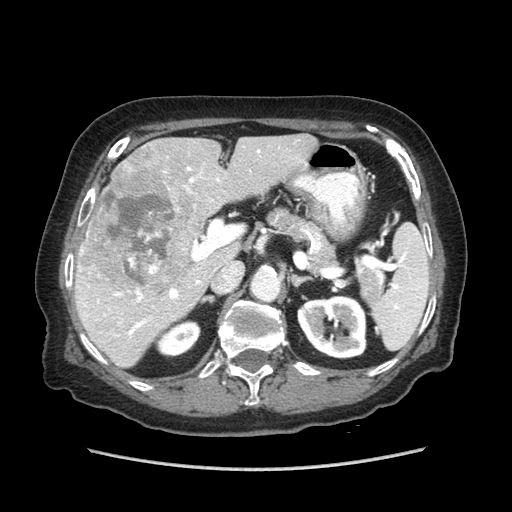
Contrast-enhanced abdominal CT (liver protocol), one axial slice. Slice 45 of 89 in the series (ordered by position). 140 kVp. Soft-tissue window (W 400 / L 40 HU). 2.5 mm slice thickness. 512 × 512 image matrix. Case-level facts recorded for this patient, not image findings: diagnosis: hepatocellular carcinoma (patient treated with transarterial chemoembolisation; whether this scan precedes or follows treatment is not stated here); TNM stage (as recorded): Stage-IIIA; Child-Pugh class: A; tumour differentiation: well differentiated; tumour size: 11 cm.
Structures marked on this image (semi-automatic segmentation, software-assisted and operator-edited):
- liver parenchyma outside the tumour (the mass and vessels are separate outlines, so this box may not span the whole liver): bounding box <74,134,316,368> (left, top, right, bottom; pixels)
- mass: <82,163,196,296>
- liver vessels: <80,150,260,337>